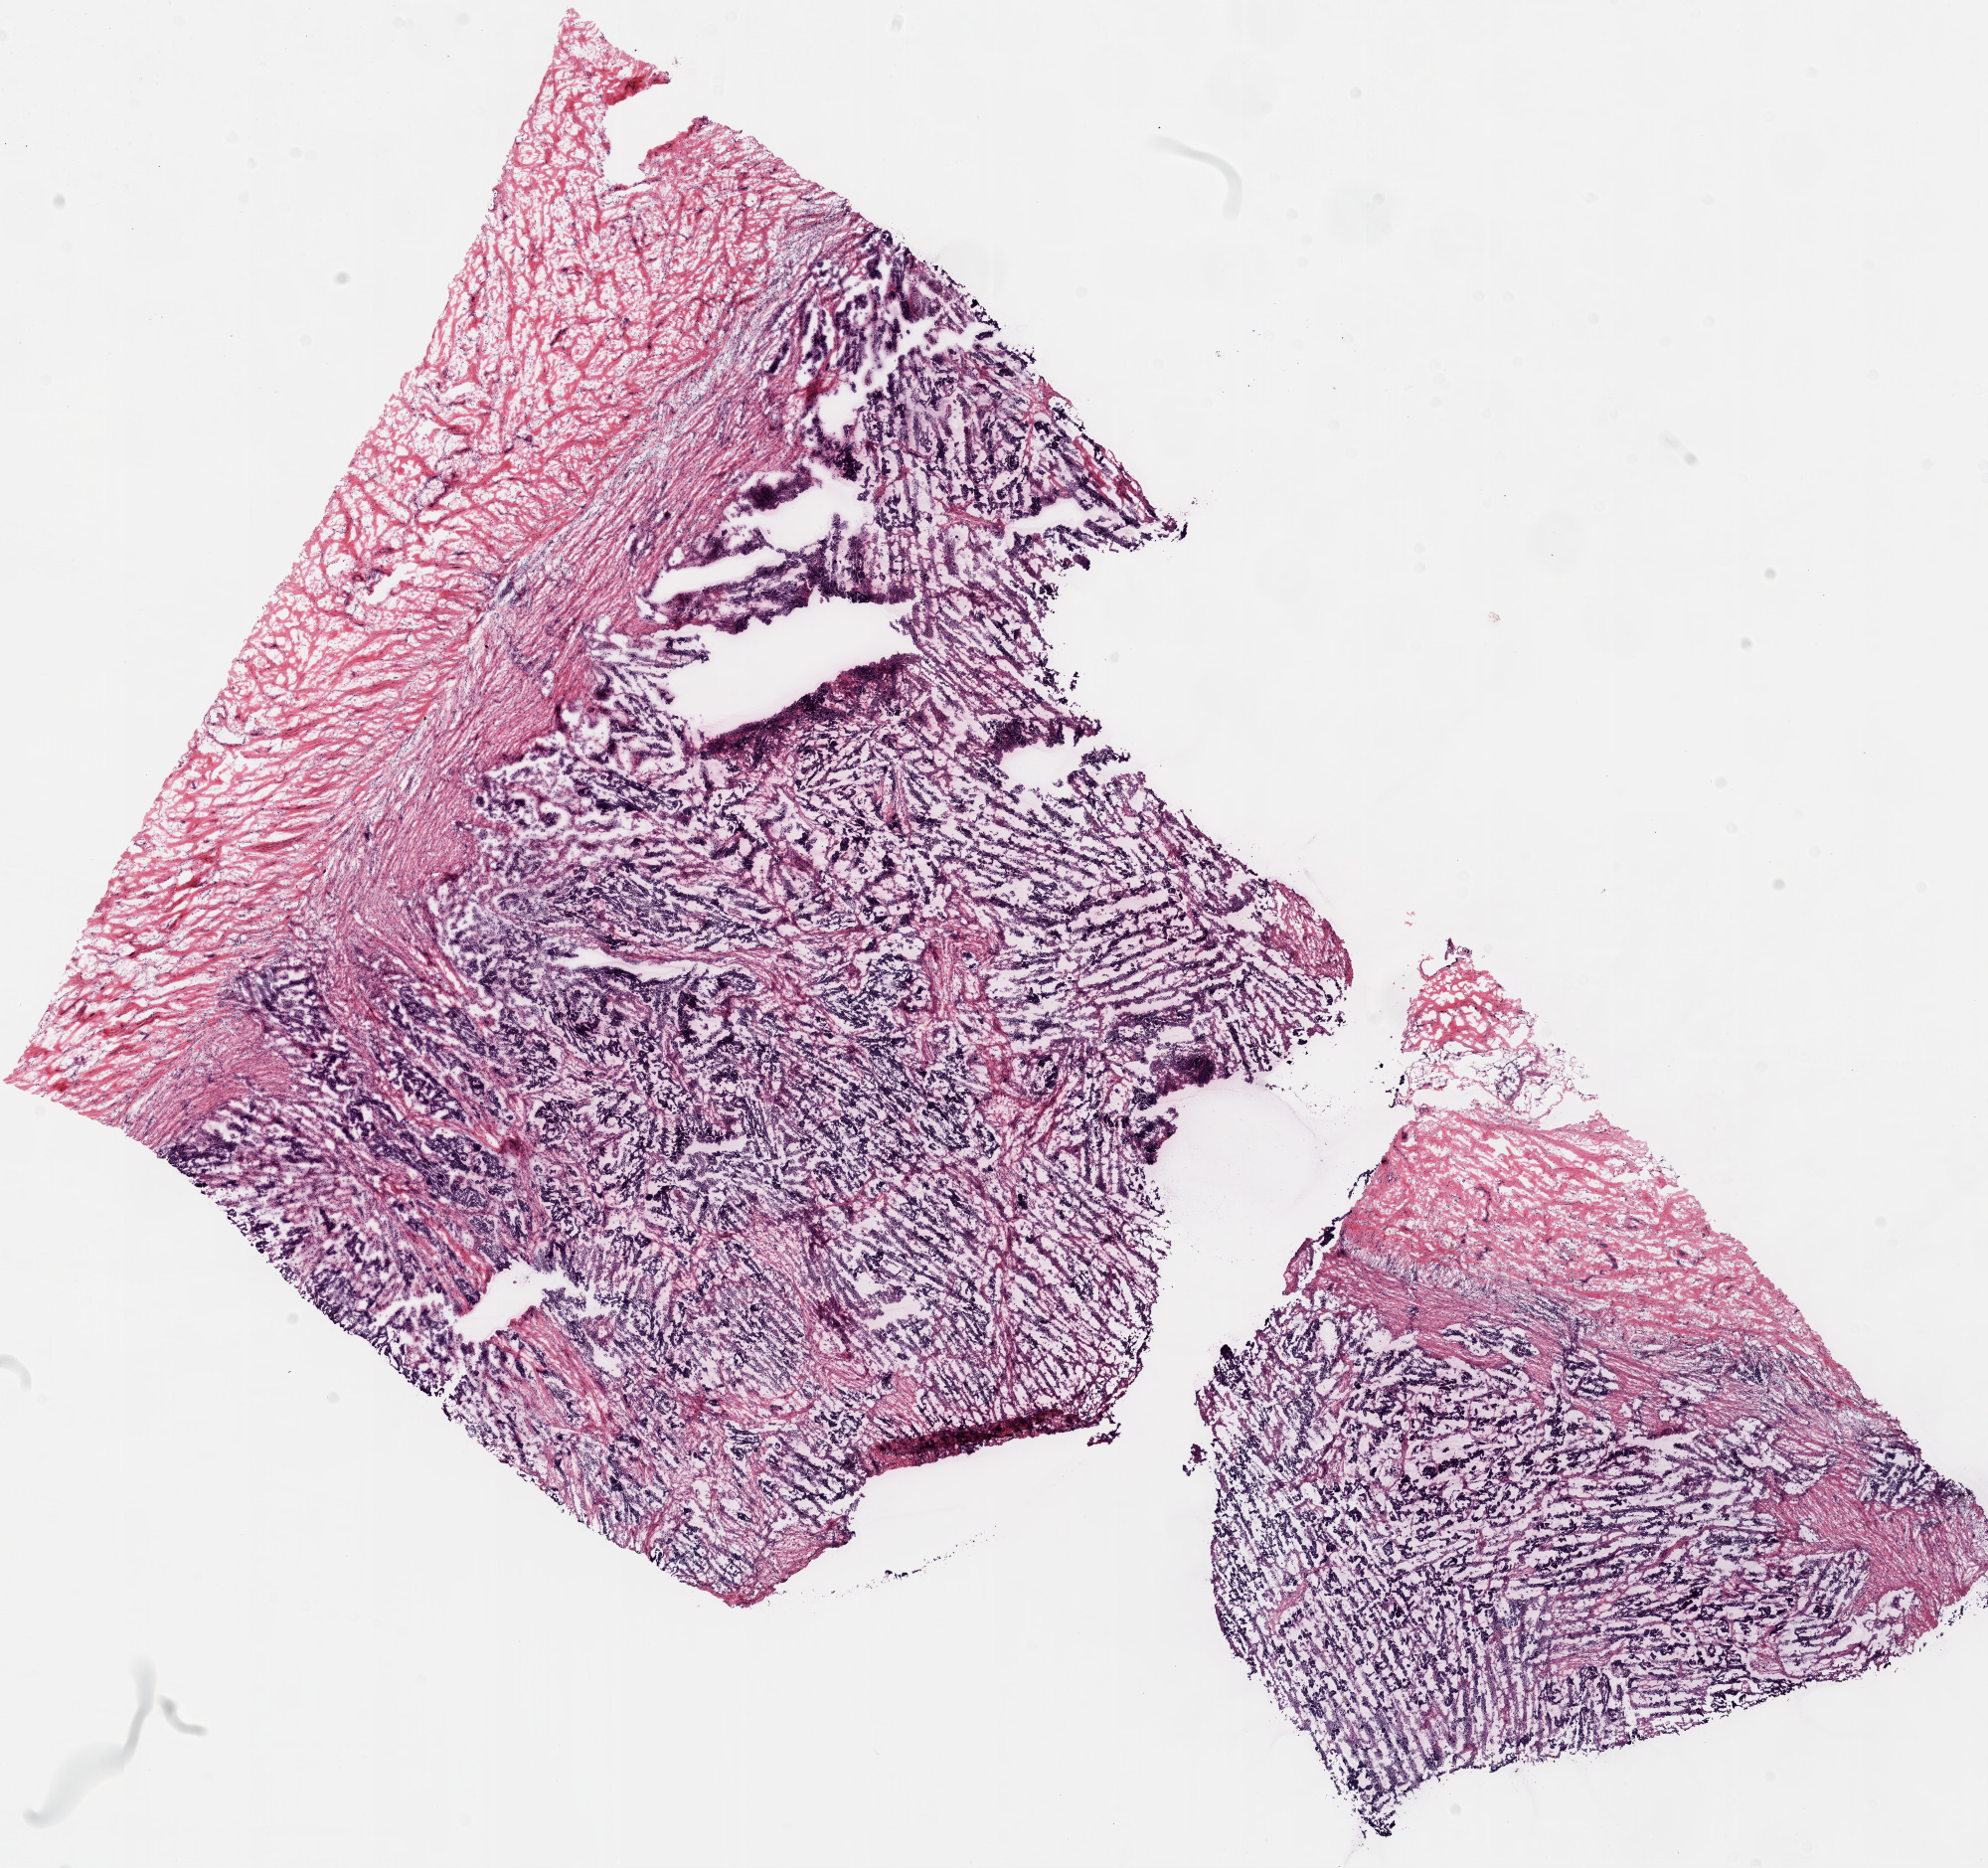
Digitized H&E-stained tissue section (whole slide), low-resolution overview of the scanned area, about 16.0 x 15.1 mm (acquisition: 20x scan), frozen section, ovary, primary tumour sample. Patient: female, age at initial diagnosis 59 years. Histologic grade: G3 (poorly differentiated). Pathologist review of this section (percent, as recorded): tumour cells 84%, tumour nuclei 85%, normal cells 0%, stromal cells 15%, necrosis 1%.
• FIGO stage: IIIC
• histologic diagnosis: Serous cystadenocarcinoma, NOS